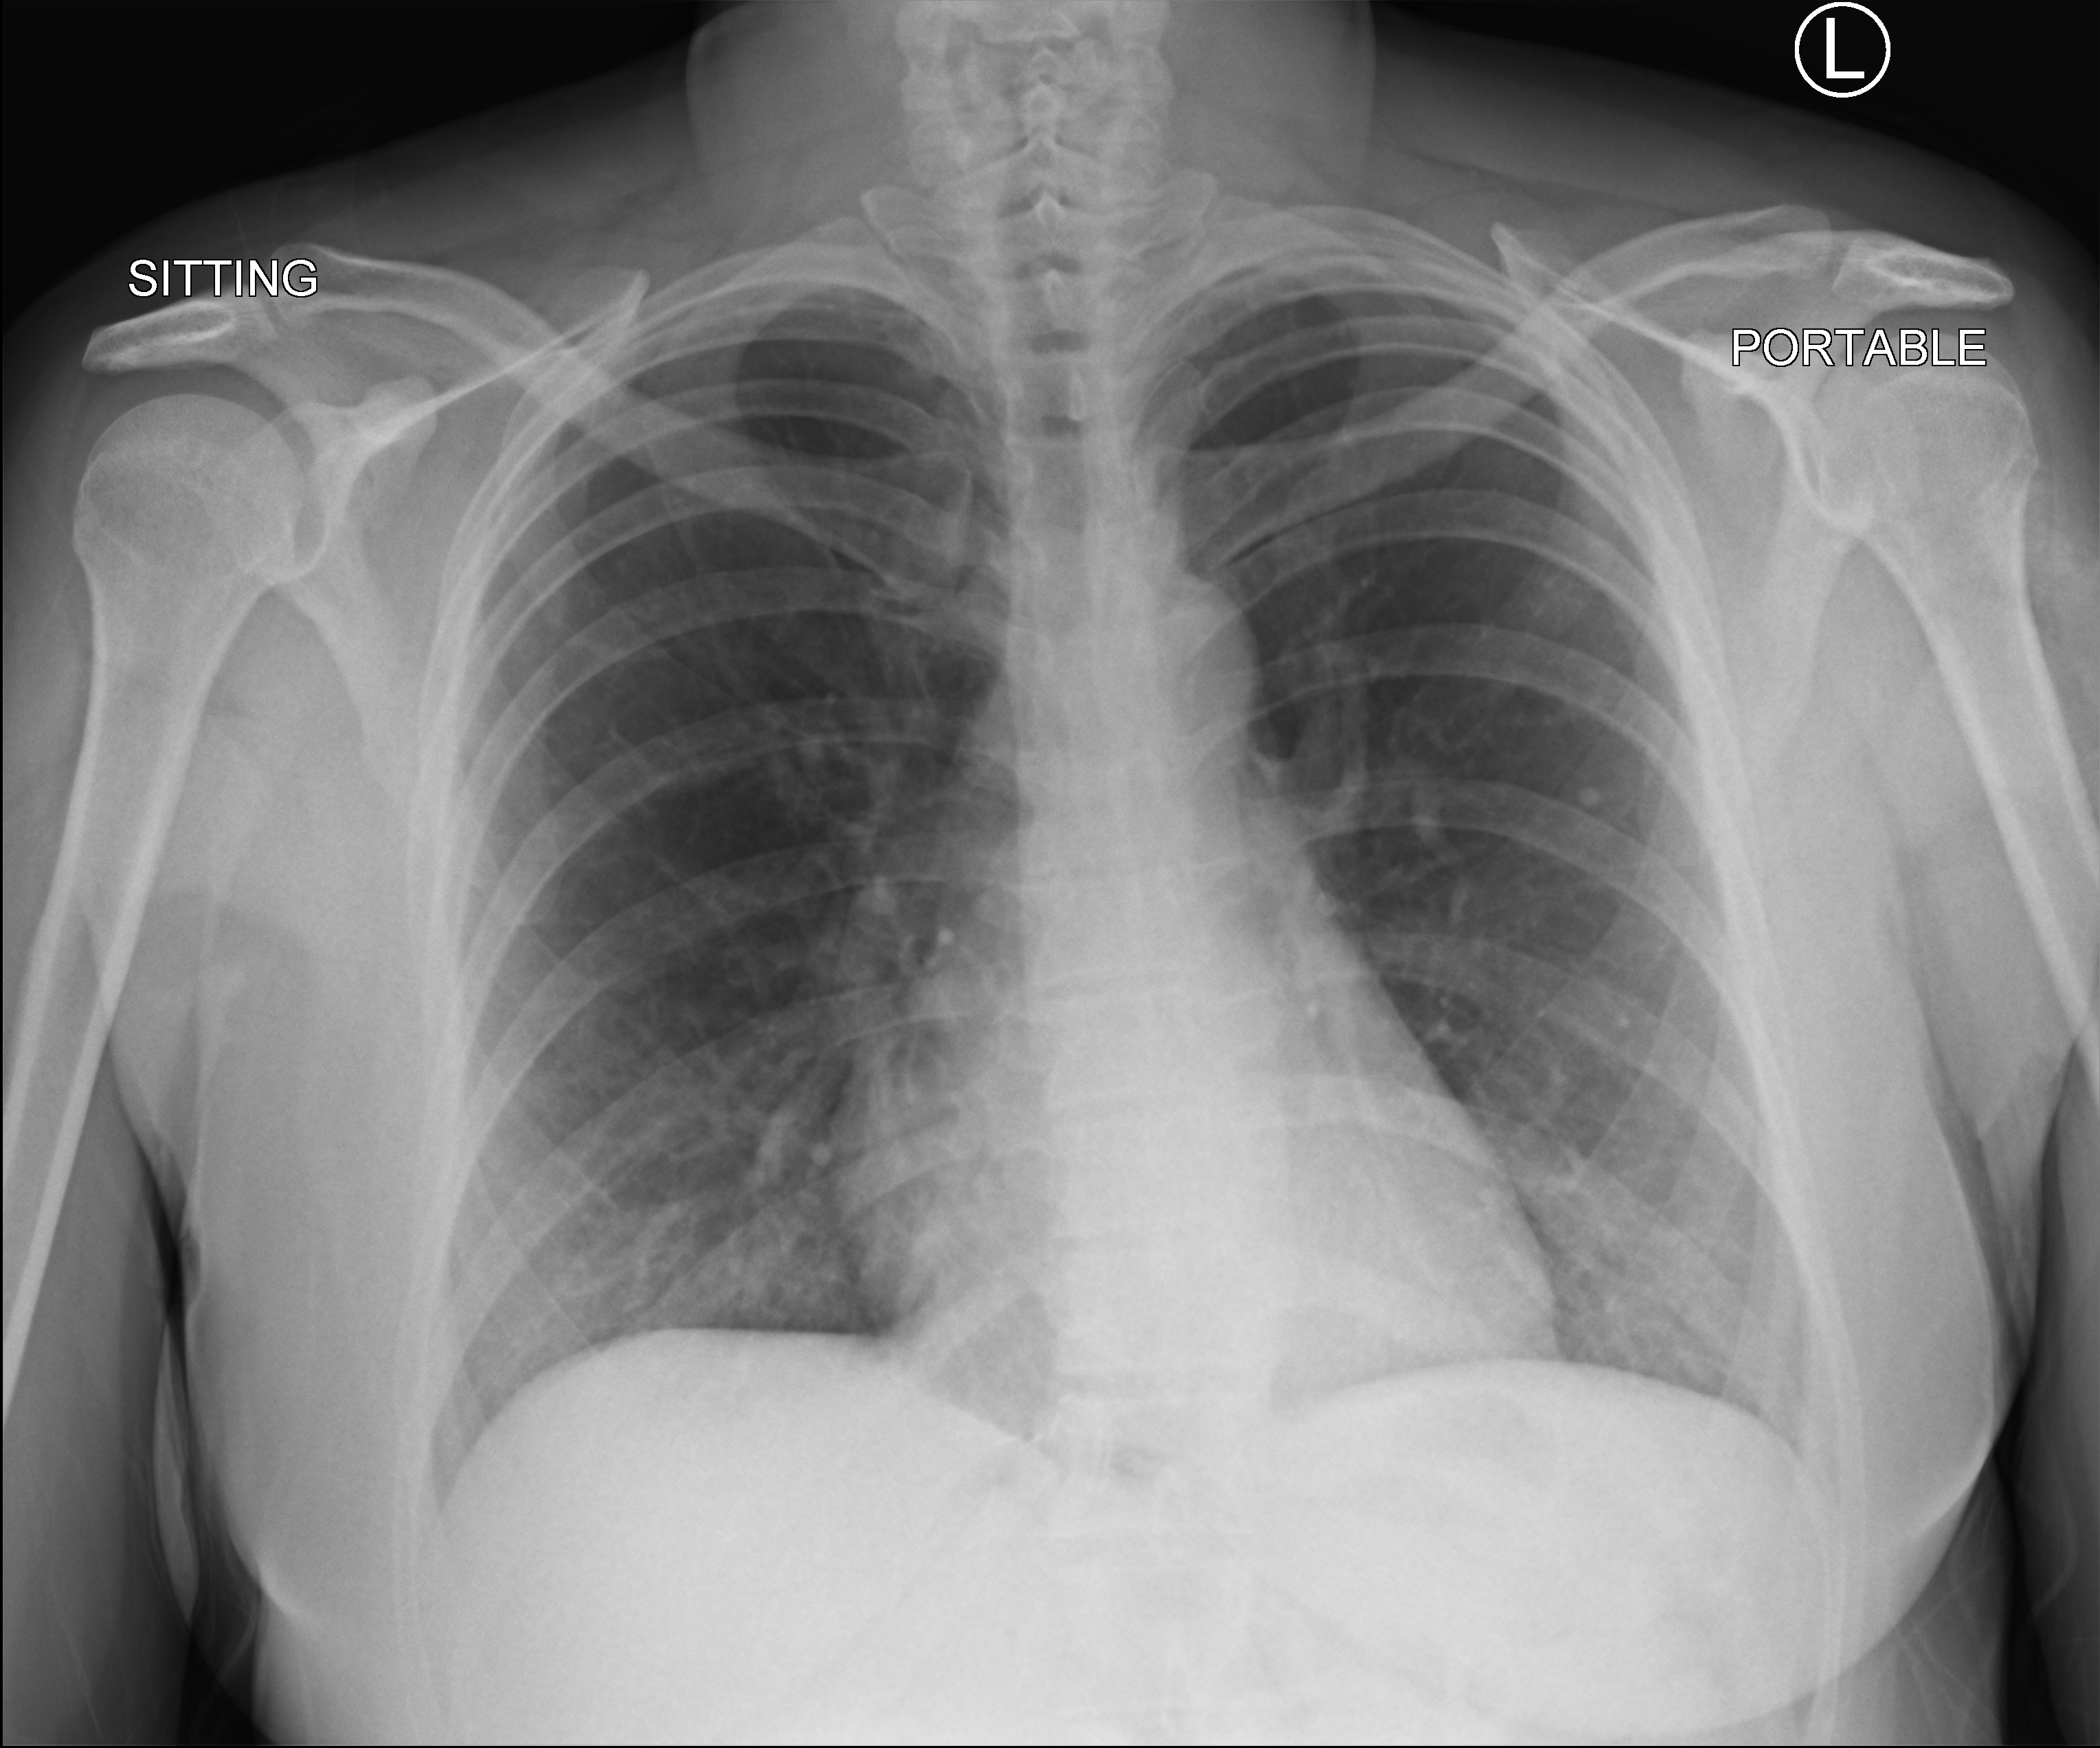
Portable chest radiograph, anteroposterior (AP) projection. Female patient hospitalised with COVID-19, age 18–59 years.
From the hospital-stay record, not from the radiograph (when in the stay this image was taken is not recorded):
- hypertension (admission record): no
- mechanically ventilated during this hospital stay: no